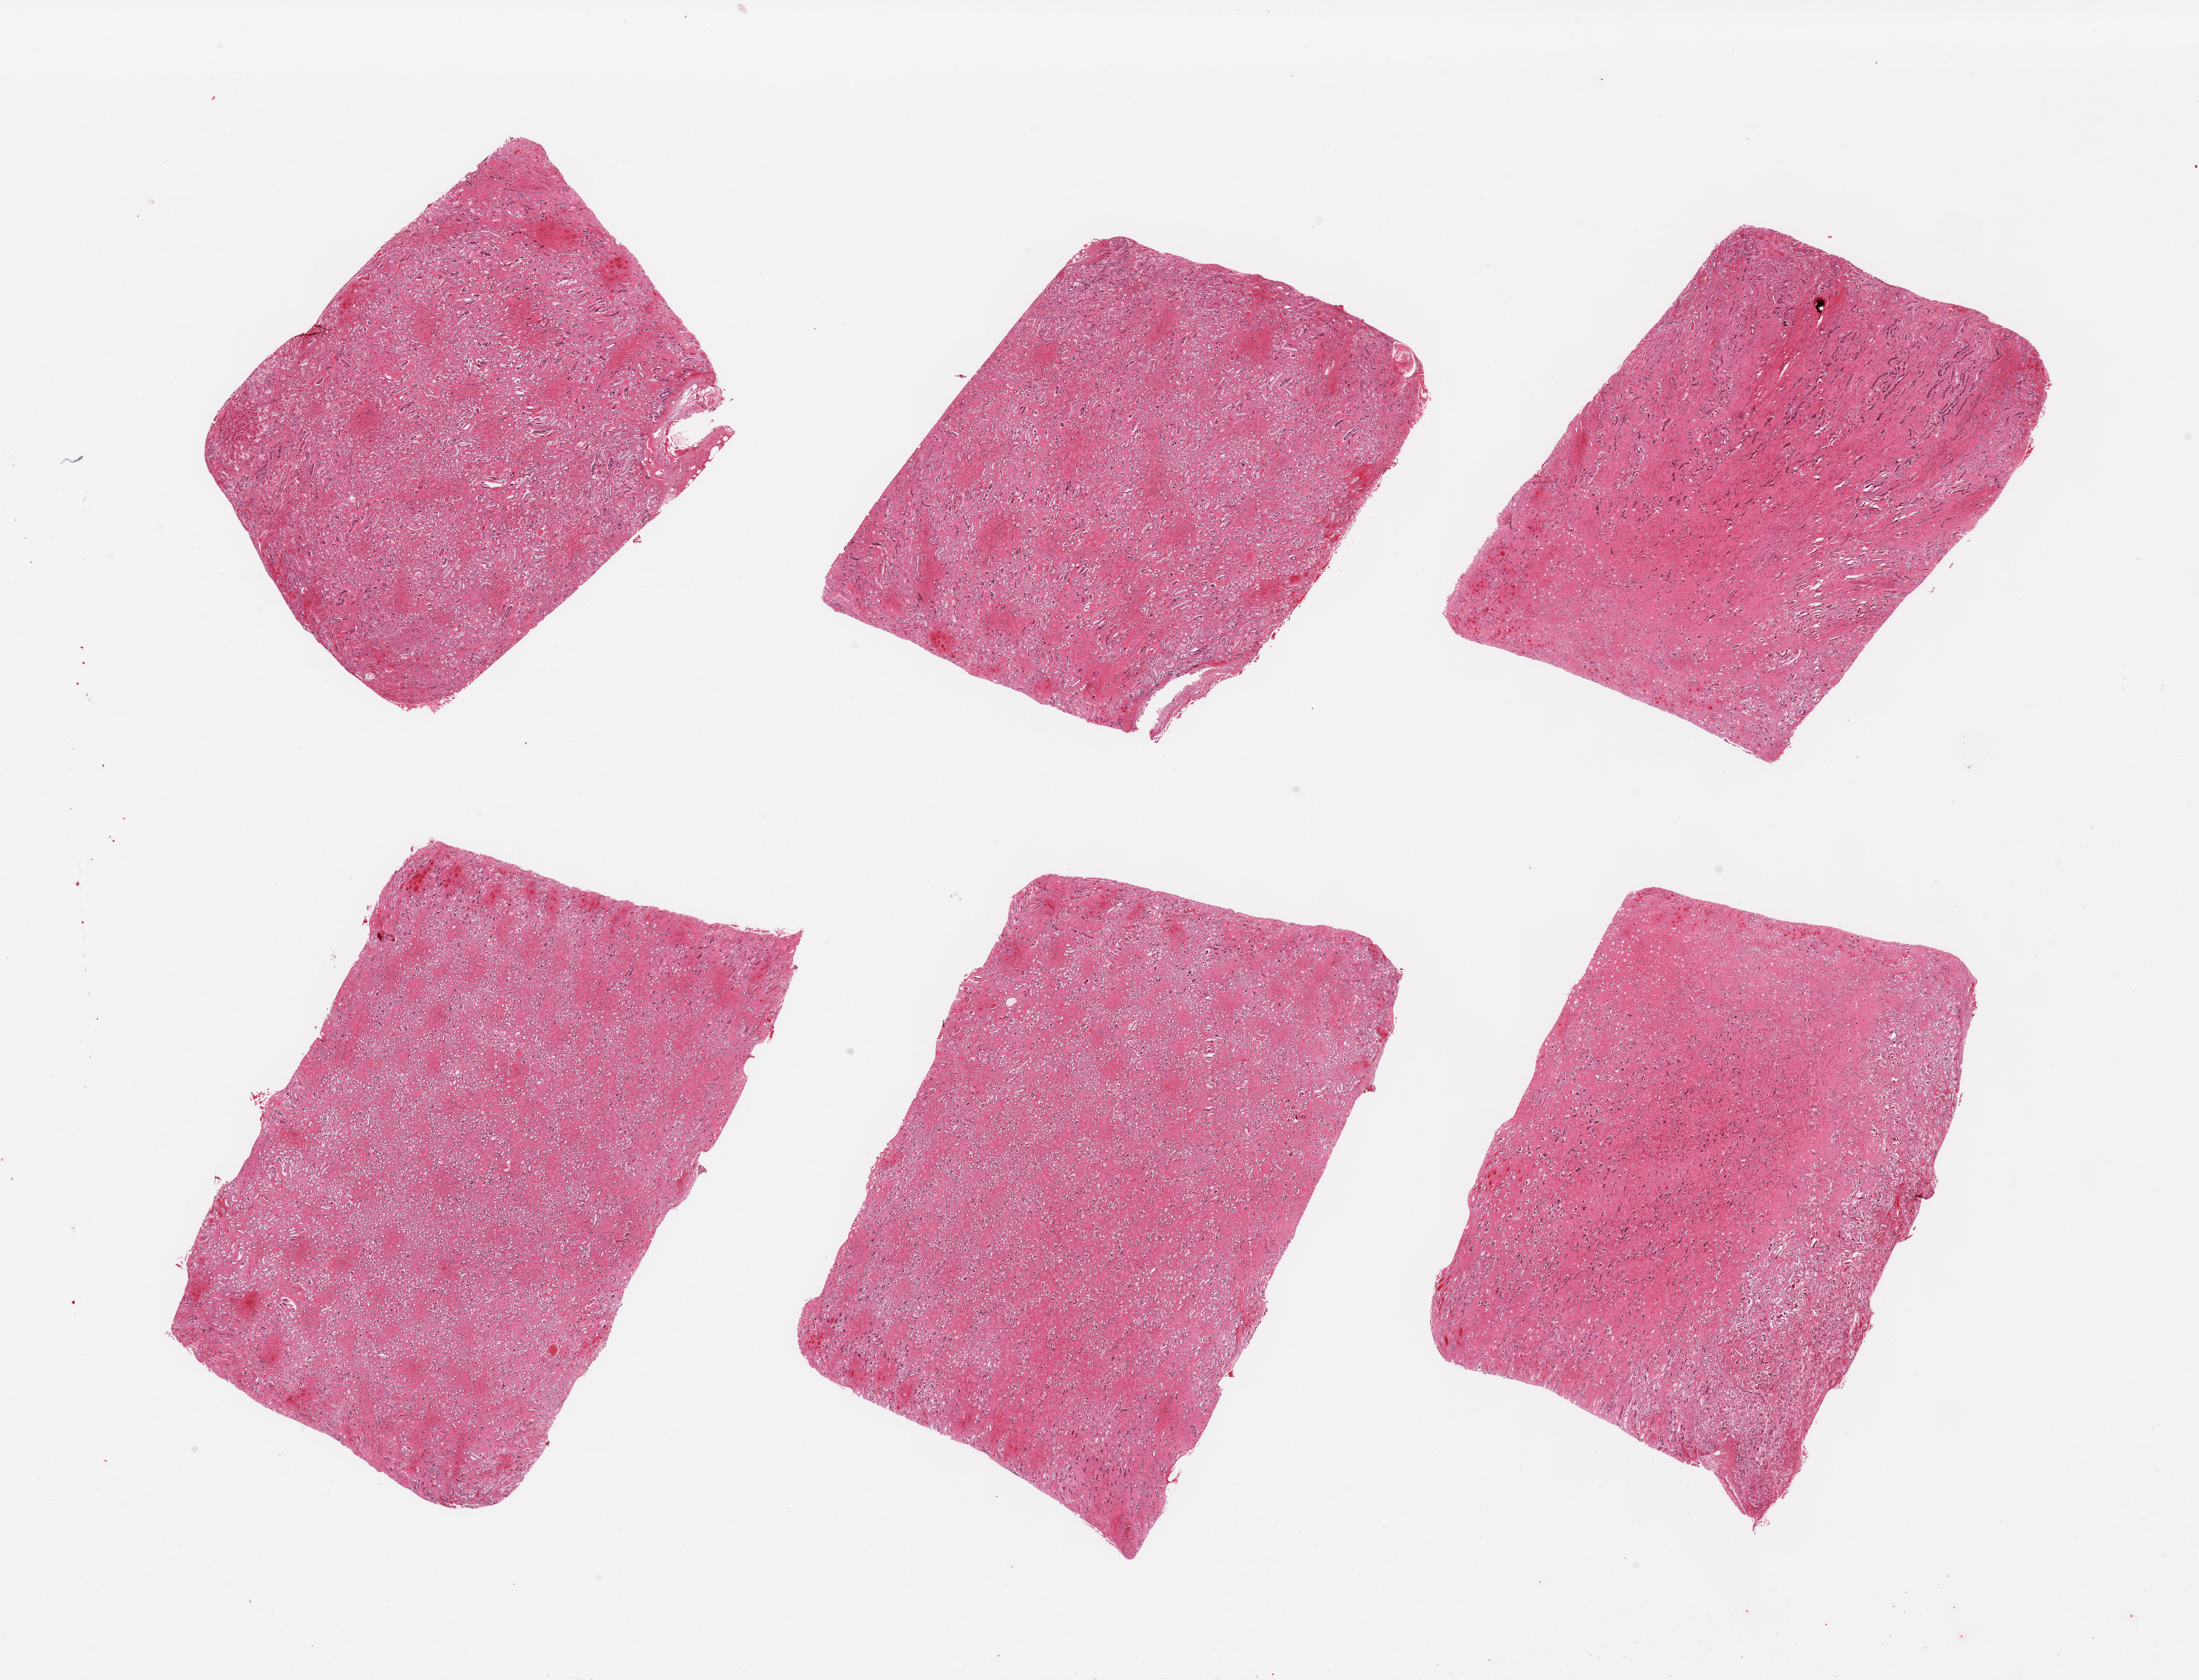
Digitized H&E-stained section — a low-resolution overview of the entire scanned area, about 28.5 x 21.8 mm. PAXgene-fixed paraffin-embedded (PFPE) section. Target tissue: renal cortex. Donor tissue sample. Male donor.
Pathologist's review note for this sample: 6 pieces, renal medulla, advanced autolysis.